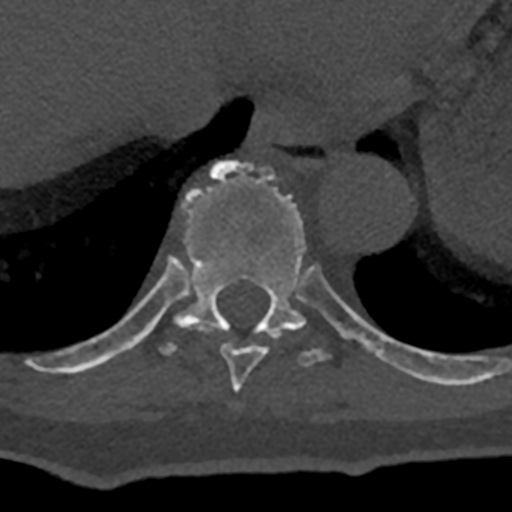
CT including the spine, one axial slice; slice 623 of 797 in the series (ordered by position); 120 kVp; bone window (W 1800 / L 400 HU); 0.5 mm slice thickness; 512 × 512 image matrix, field of view 160 × 160 mm. Male patient, age 74 years. Case-level facts recorded for this patient, not image findings: primary cancer: renal; vertebrae with lytic lesions (as recorded): T10, L1, L2, L3, L4, L5.
Structures marked on this image (semi-automatic segmentation, software-assisted and operator-edited):
- T10 vertebra: bounding box [x1, y1, x2, y2] px = [70, 161, 432, 383]
- T9 vertebra: [180, 323, 280, 392]